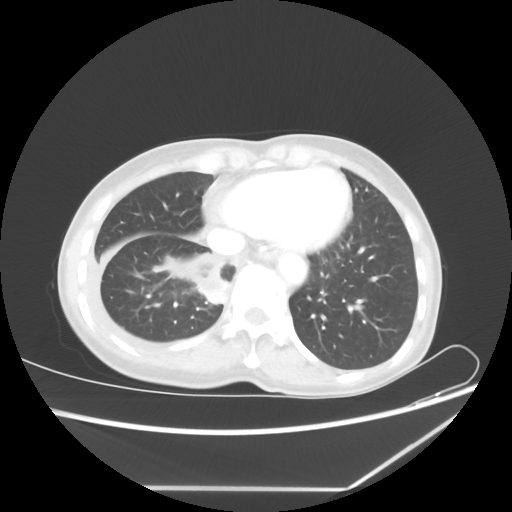
Chest CT, one axial slice. Slice 16 of 60 in the series (ordered by position). Reconstruction kernel STANDARD. 80 kVp. Lung window (W 1500 / L -600 HU). 5 mm slice thickness. 512 × 512 image matrix, field of view 364 × 364 mm. Female patient, age 59 years. Case-level facts recorded for this patient, not image findings: clinical TNM (as recorded): T1c N1 M1.
Structures marked on this image (rectangle marked by the reading radiologist):
- lung tumour (recorded histology: adenocarcinoma): box from (x=195, y=280) to (x=228, y=305) px